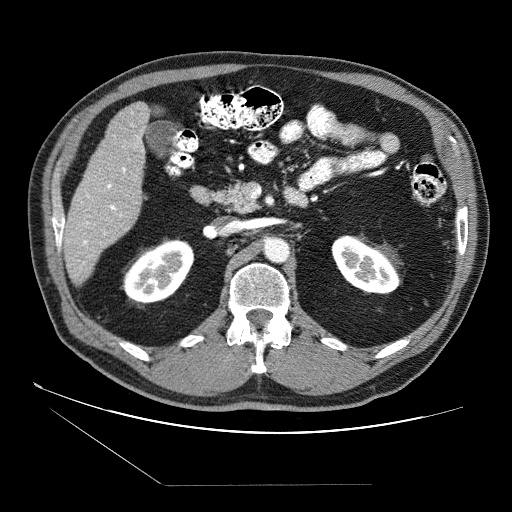
Contrast-enhanced abdominal CT (liver protocol), one axial slice. Slice 25 of 87 in the series (ordered by position). 120 kVp. Soft-tissue window (W 400 / L 40 HU). 2.5 mm slice thickness. 512 × 512 image matrix. Case-level facts recorded for this patient, not image findings: diagnosis: hepatocellular carcinoma (patient treated with transarterial chemoembolisation; whether this scan precedes or follows treatment is not stated here); TNM stage (as recorded): Stage-II; Child-Pugh class: B.
Annotated regions visible in this slice (semi-automatic segmentation, software-assisted and operator-edited):
- liver parenchyma outside the tumour (the mass and vessels are separate outlines, so this box may not span the whole liver): bounding box (x1, y1, x2, y2) in pixels: (64, 102, 150, 284)
- liver vessels: (82, 112, 143, 264)